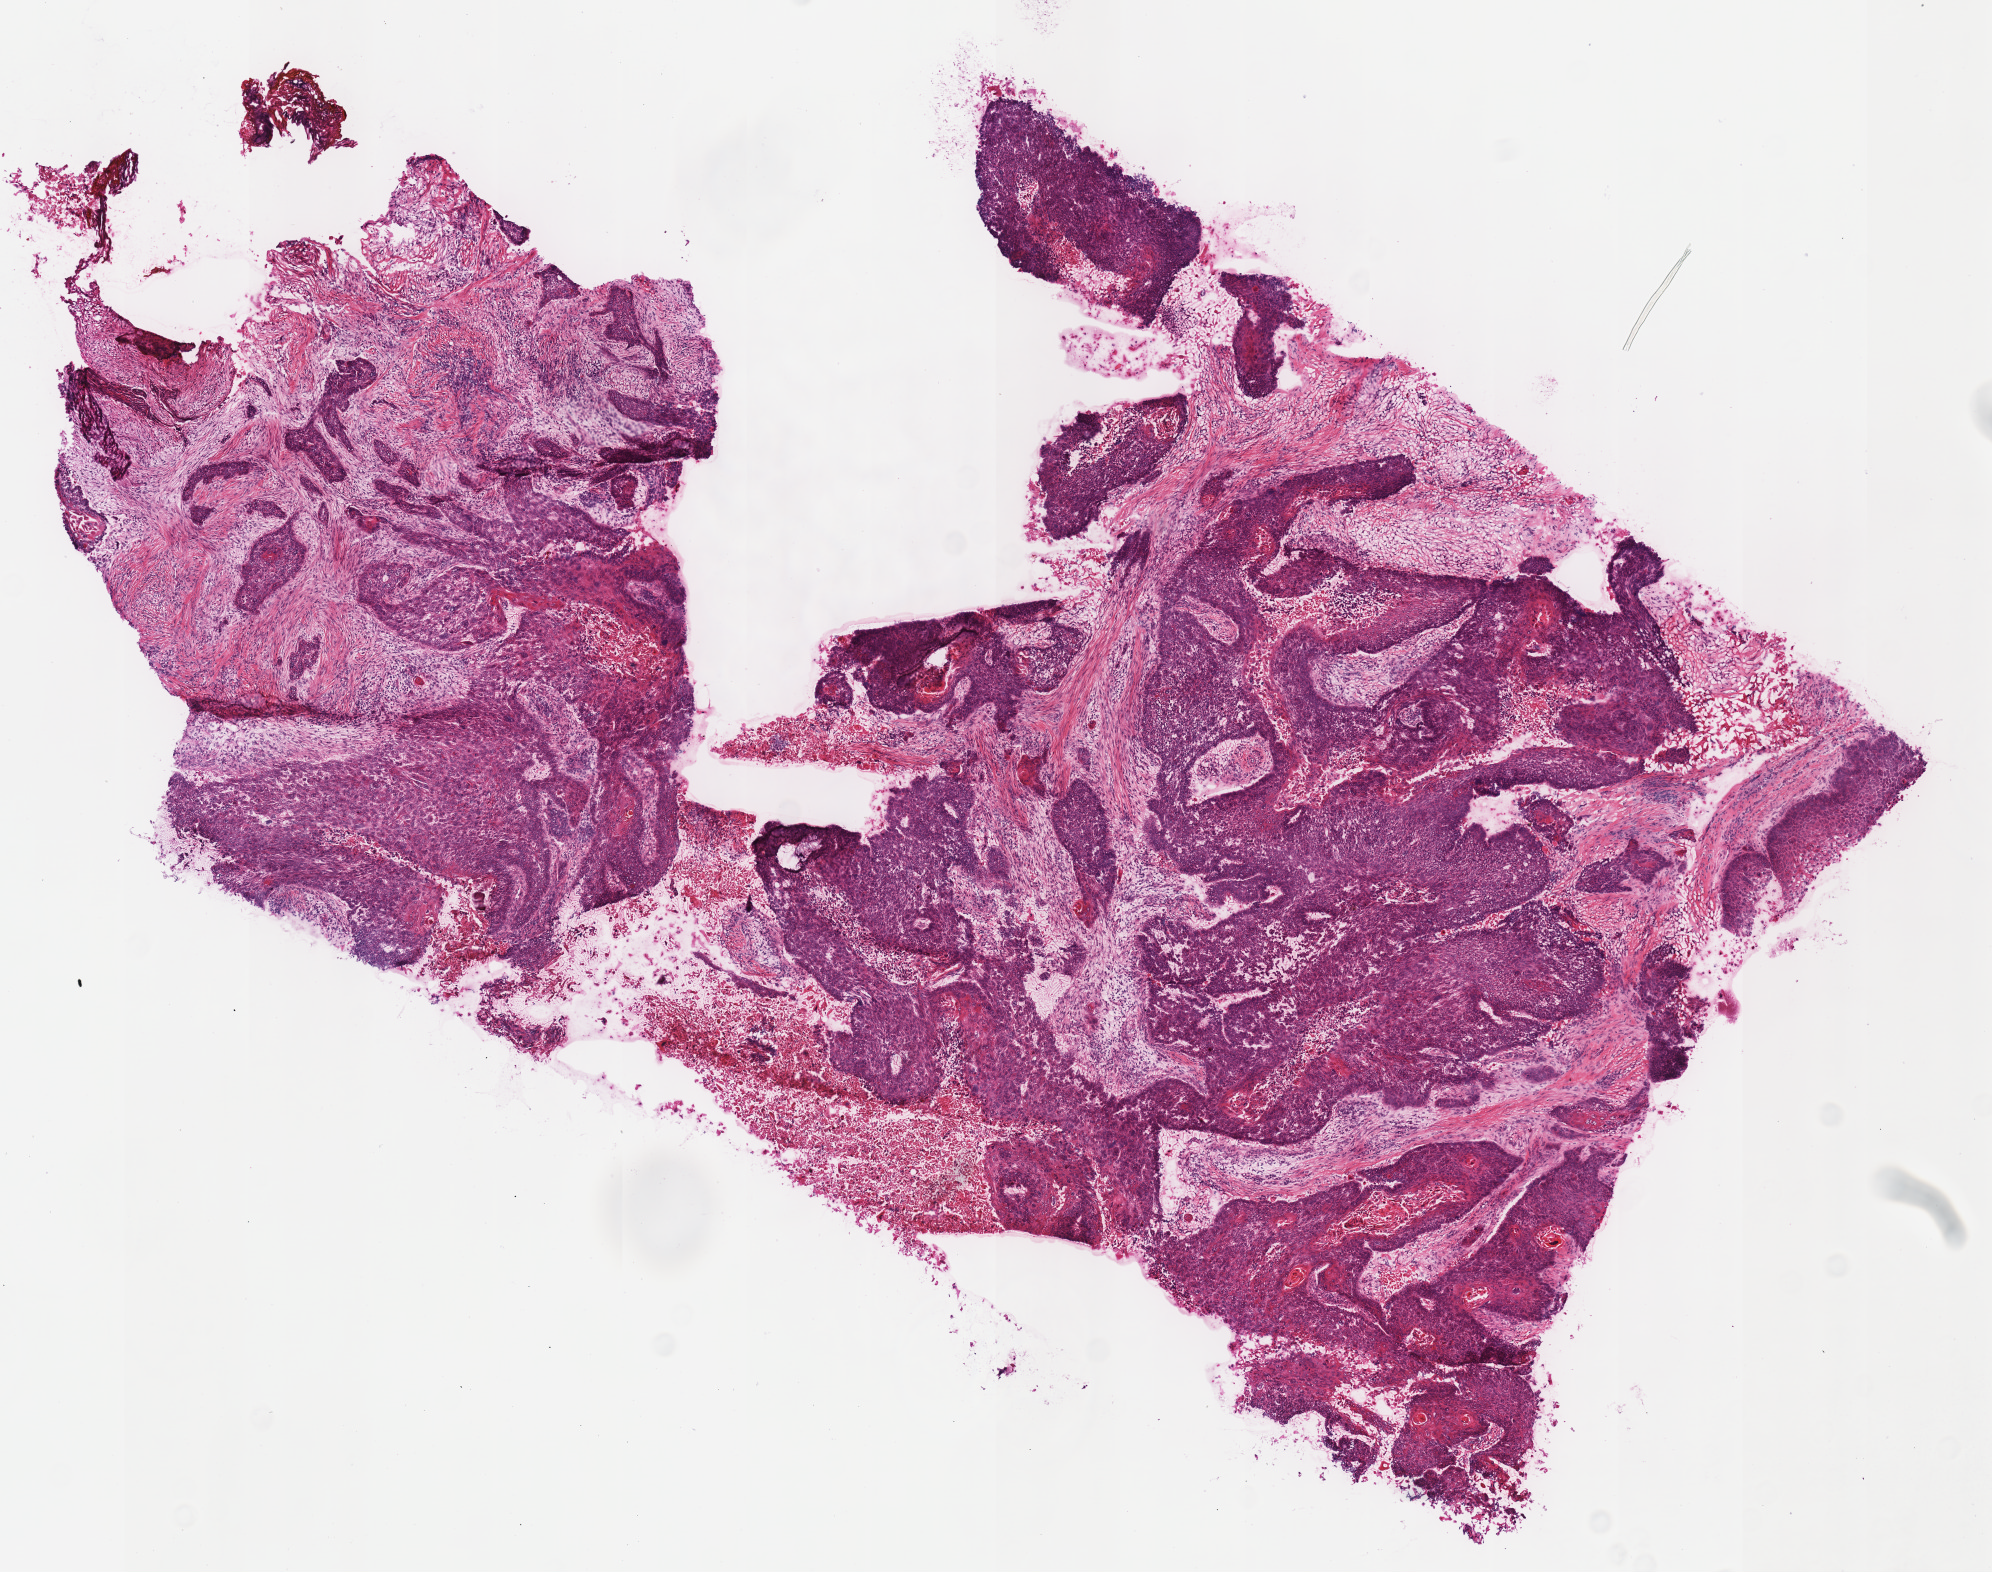
Digitized H&E-stained tissue section (whole slide), a low-resolution overview of the entire scanned area, about 7.8 x 6.2 mm (from a 40x scan). Frozen section from the top of the tissue portion. Primary tumour sample from the head and neck. Patient: male, age at initial diagnosis 84 years. Histologic grade: G2 (moderately differentiated). Composition of this section per pathologist review: tumour cells 85%, tumour nuclei 80%, normal cells 0%, stromal cells 15%, necrosis 0%. Inflammatory infiltration, as recorded: lymphocyte infiltration 10%, monocyte infiltration 0%, neutrophil infiltration 0%.
Laterality: right. Pathologic diagnosis: Squamous cell carcinoma, NOS (floor of mouth, NOS). AJCC pathologic stage: III (7th edition).